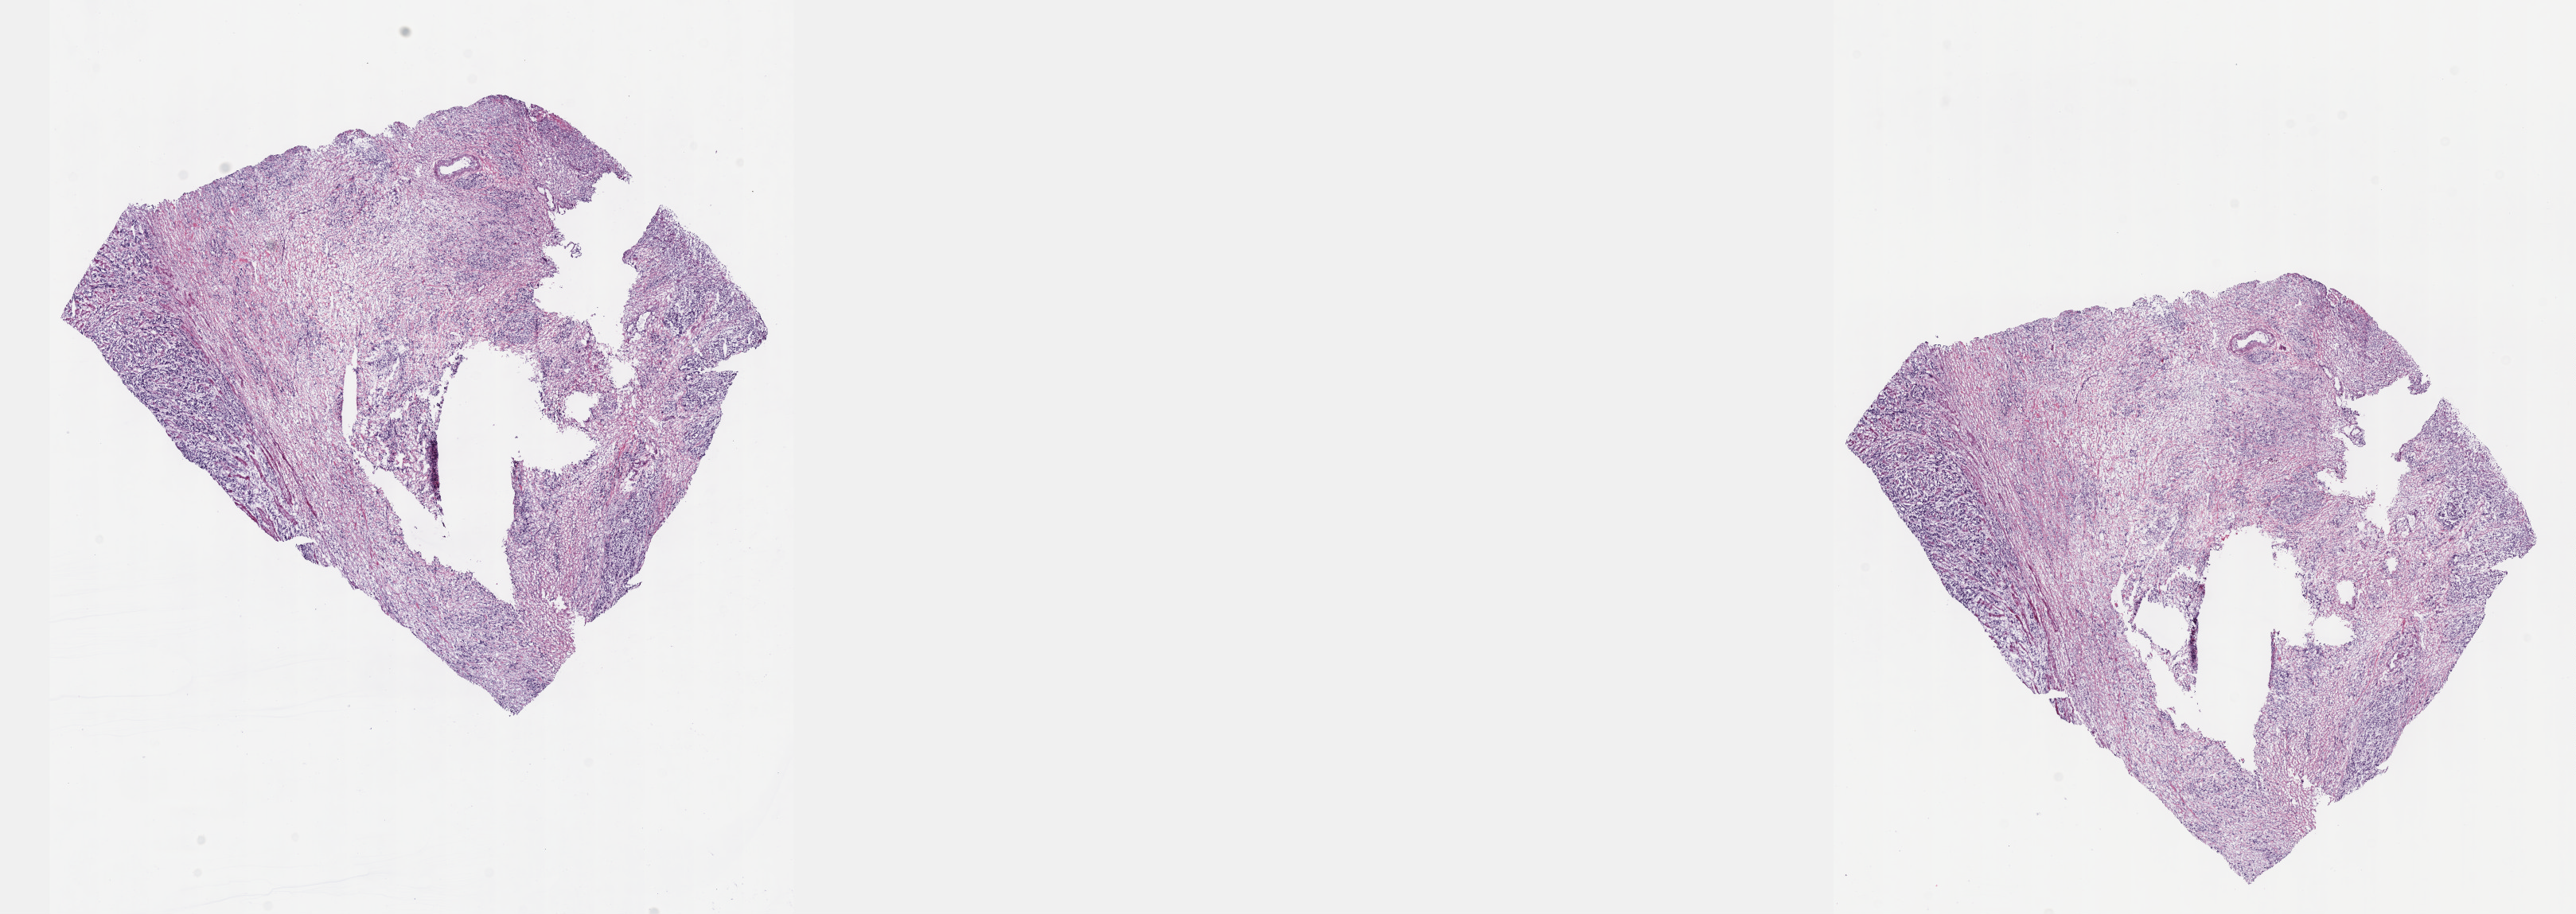
Whole-slide histology image, H&E, a low-resolution overview of the entire scanned area, about 26.2 x 9.3 mm (slide scanned at 40x). Frozen section. Sample: primary tumour, esophagus. Male, age 56 years at initial diagnosis. Histologic grade: GX (grade cannot be assessed). Slide review estimates, as recorded: tumour cells 100%, tumour nuclei 70%, normal cells 0%, stromal cells 0%, necrosis 0%. Infiltration values recorded for this section: lymphocyte infiltration 0%, monocyte infiltration 0%, neutrophil infiltration 0%.
AJCC pathologic stage: III (6th edition). TNM: T3 N1 M0. Lymph nodes positive (case pathology): 4 of 9 examined. Histologic diagnosis: Adenocarcinoma, NOS (lower third of esophagus).